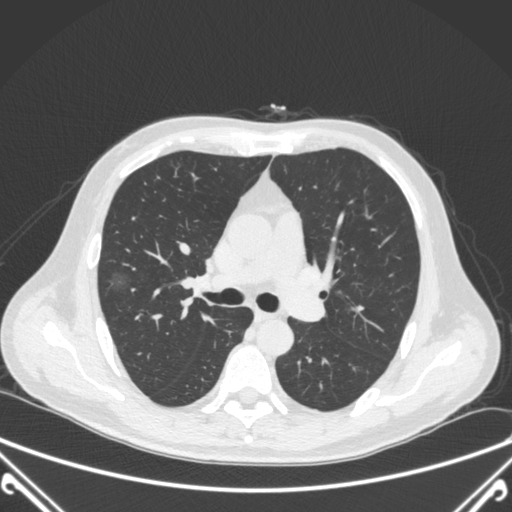
Chest CT, one axial slice; 120 kVp; lung window (W 1500 / L -600 HU); 1 mm slice thickness; 512 × 512 image matrix, field of view 380 × 380 mm. Patient: male, 64 years. Case-level facts recorded for this patient, not image findings: clinical TNM (as recorded): T1c N0 M0; histopathological grade: G2.
Outlined on this slice (rectangle marked by the reading radiologist):
- lung tumour (recorded histology: adenocarcinoma): box from (x=104, y=266) to (x=137, y=300) px